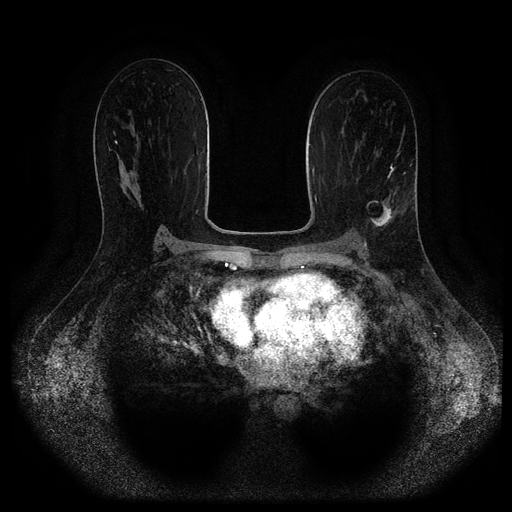
Breast MRI (dynamic contrast-enhanced, multi-phase), one axial slice. Slice 60 of 116 in the series (ordered by position). Dynamic contrast-enhanced series, time point 2 of 5 at this slice position (early post-contrast). 1.5 T. TE 2.6 ms, TR 5.3 ms. 512 × 512 image matrix, field of view 370 × 370 mm. Female patient, age 45 years.
Structures marked on this image (semi-automatic segmentation, software-assisted and operator-edited):
- breast lesion (labelled 'tumour' in the annotation; benign lesions carry a separate 'benign' label): bounding box <368,201,395,230> (left, top, right, bottom; pixels)